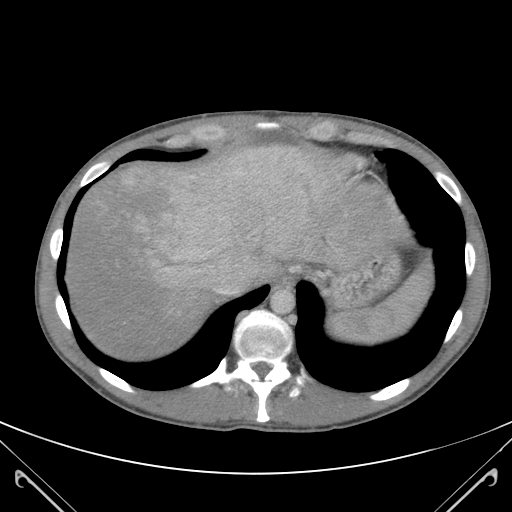
Contrast-enhanced abdominal CT (liver protocol), one axial slice. Slice 100 of 118 in the series (ordered by position). 120 kVp. Soft-tissue window (W 400 / L 40 HU). 3 mm slice thickness. 512 × 512 image matrix, field of view 380 × 380 mm. Case-level facts recorded for this patient, not image findings: diagnosis: hepatocellular carcinoma (patient treated with transarterial chemoembolisation; whether this scan precedes or follows treatment is not stated here); TNM stage (as recorded): Stage-IIIB; Child-Pugh class: A; tumour nodularity: uninodular.
Structures marked on this image (semi-automatically segmented with operator editing):
- abdominal aorta: bounding box <273,289,295,312> (left, top, right, bottom; pixels)
- liver parenchyma outside the tumour (the mass and vessels are separate outlines, so this box may not span the whole liver): <72,153,338,356>
- mass: <93,143,333,301>
- liver vessels: <215,256,249,295>